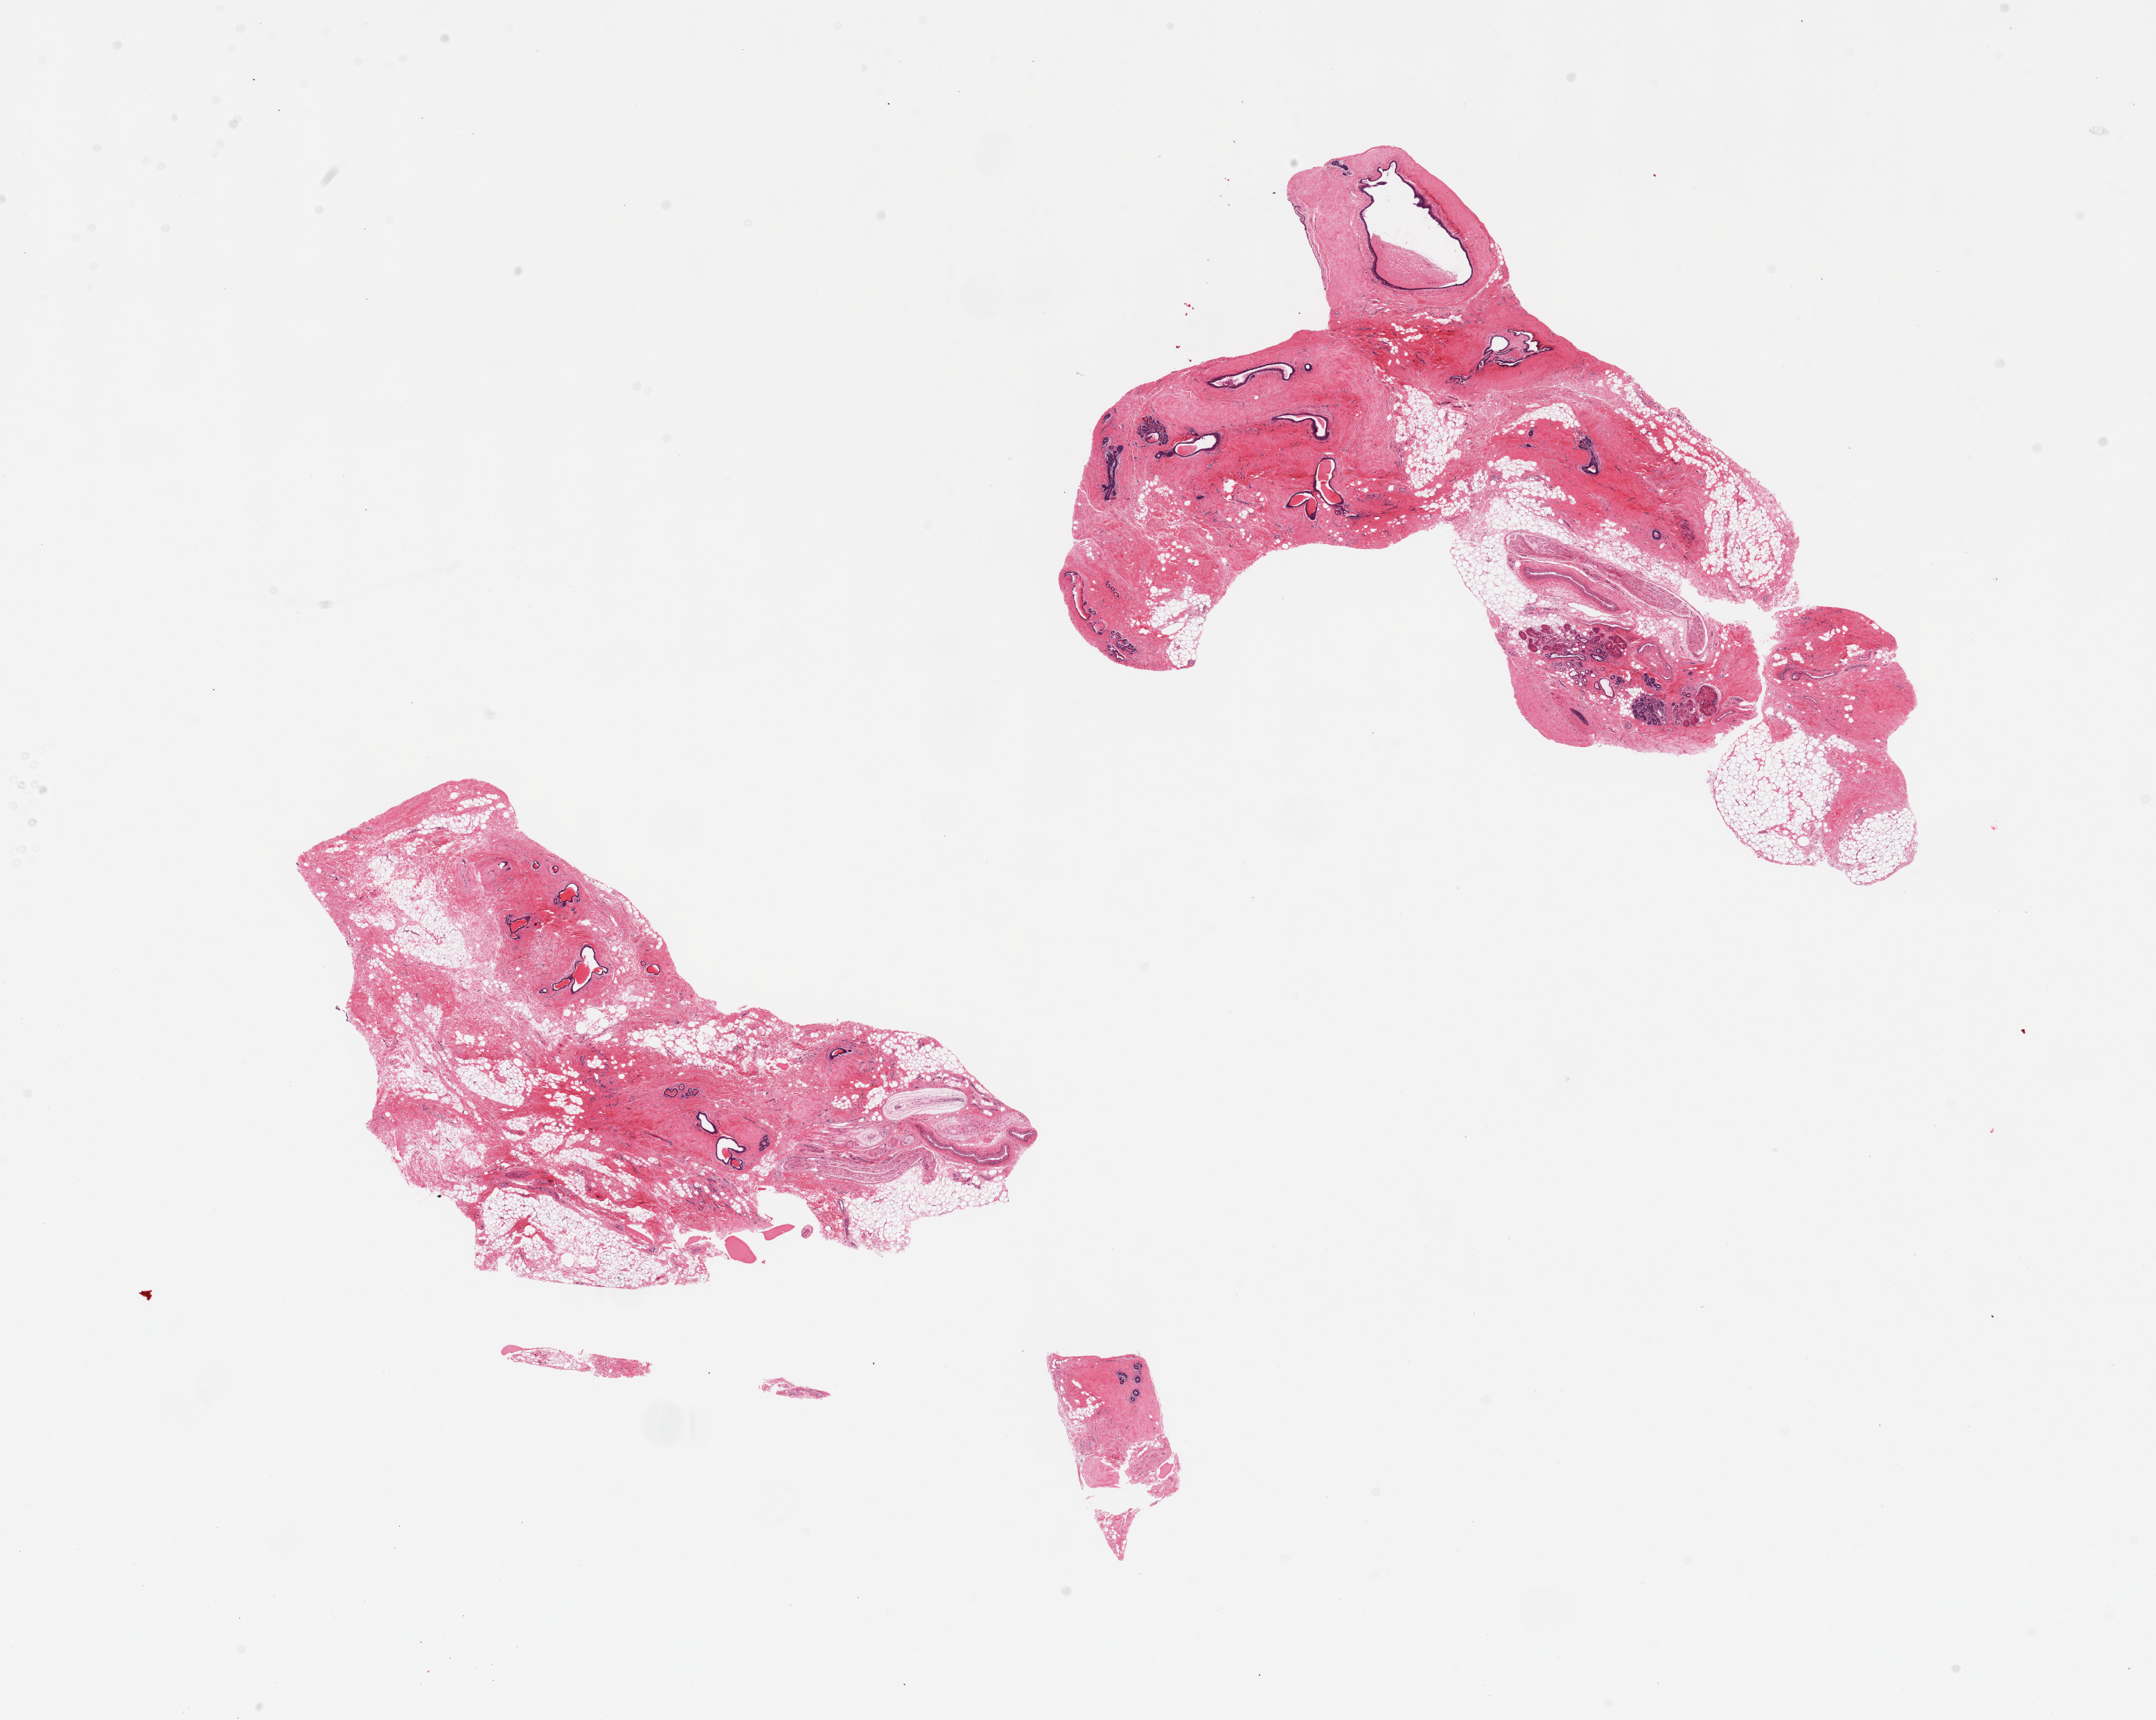
Haematoxylin and eosin whole-slide image, a low-resolution overview of the entire scanned area, about 24.6 x 19.6 mm (from a 20x scan). PAXgene-fixed, paraffin-embedded tissue. Target tissue: breast. Donor tissue sample. Donor: female.
- review note (as recorded): 2 pieces; fibrocystic disease